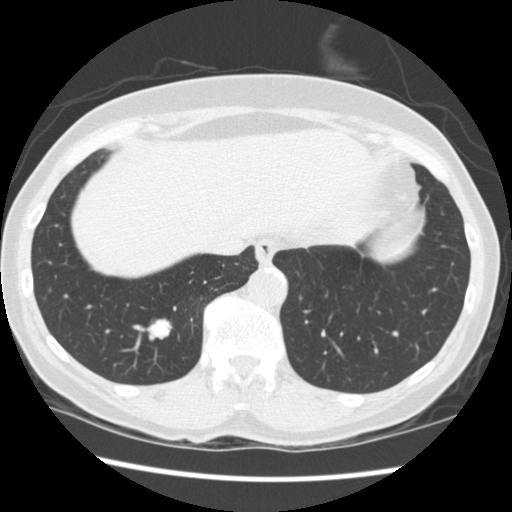
Low-dose screening chest CT, one axial slice; reconstruction kernel STANDARD; 120 kVp; lung window (W 1500 / L -600 HU); 512 × 512 image matrix.
Annotated regions visible in this slice (outlined manually by an expert reader):
- lesion 1 (tumor, lower lobe of right lung): bounding box [x1, y1, x2, y2] px = [147, 319, 172, 339]